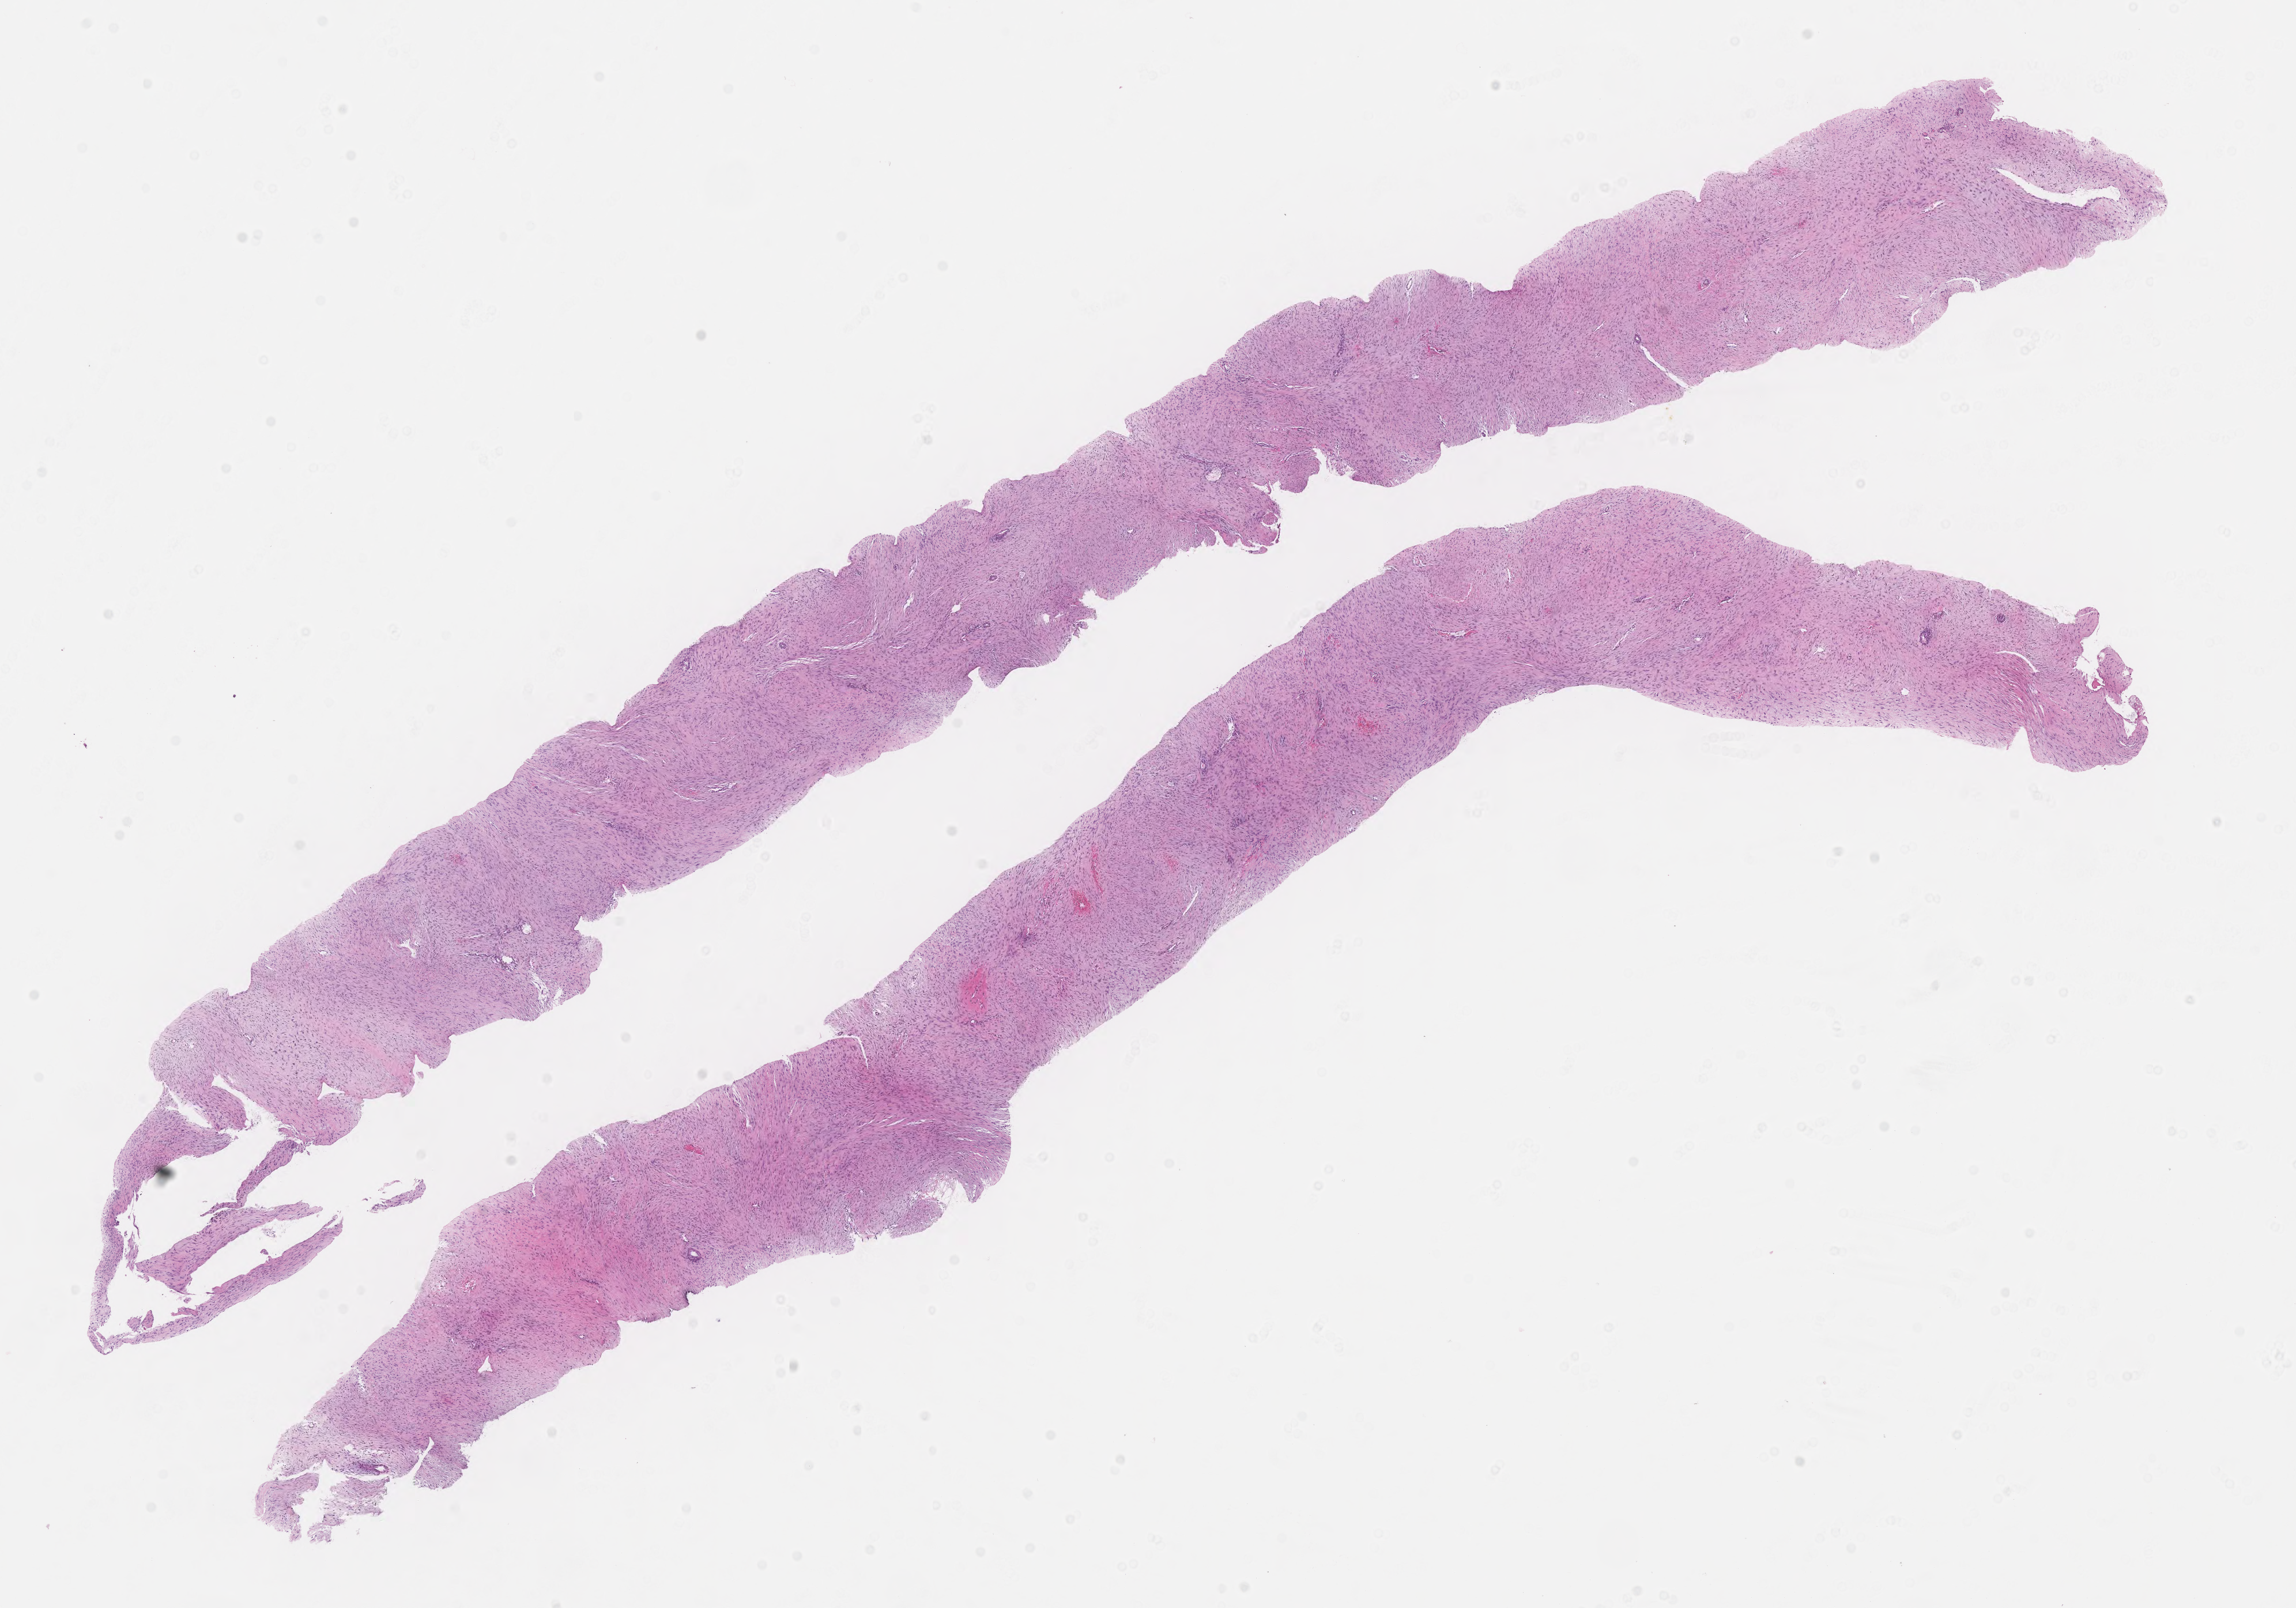
Whole-slide image, hematoxylin and eosin (H&E) stain of tumor tissue from the peritoneum — low-resolution overview of the scanned area, about 16.1 x 11.3 mm; formalin-fixed, paraffin-embedded (FFPE) tissue. Patient: male, age 212 months (17 years 8 months).
• diagnosis: Aggressive fibromatosis